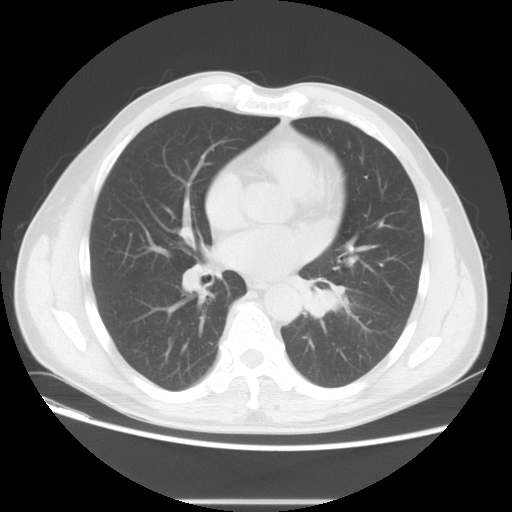
Chest CT, one axial slice; position 27 of 59 along the scan axis; reconstruction kernel STANDARD; lung window (W 1500 / L -600 HU); 5 mm slice thickness; 512 × 512 image matrix, field of view 378 × 378 mm. Patient: male, 59 years. From the clinical record (not read from this slice): clinical TNM (as recorded): T2 N3 M0.
Structures marked on this image (rectangle marked by the reading radiologist):
- lung tumour (recorded histology: small cell carcinoma): bounding box <293,270,355,339> (left, top, right, bottom; pixels)